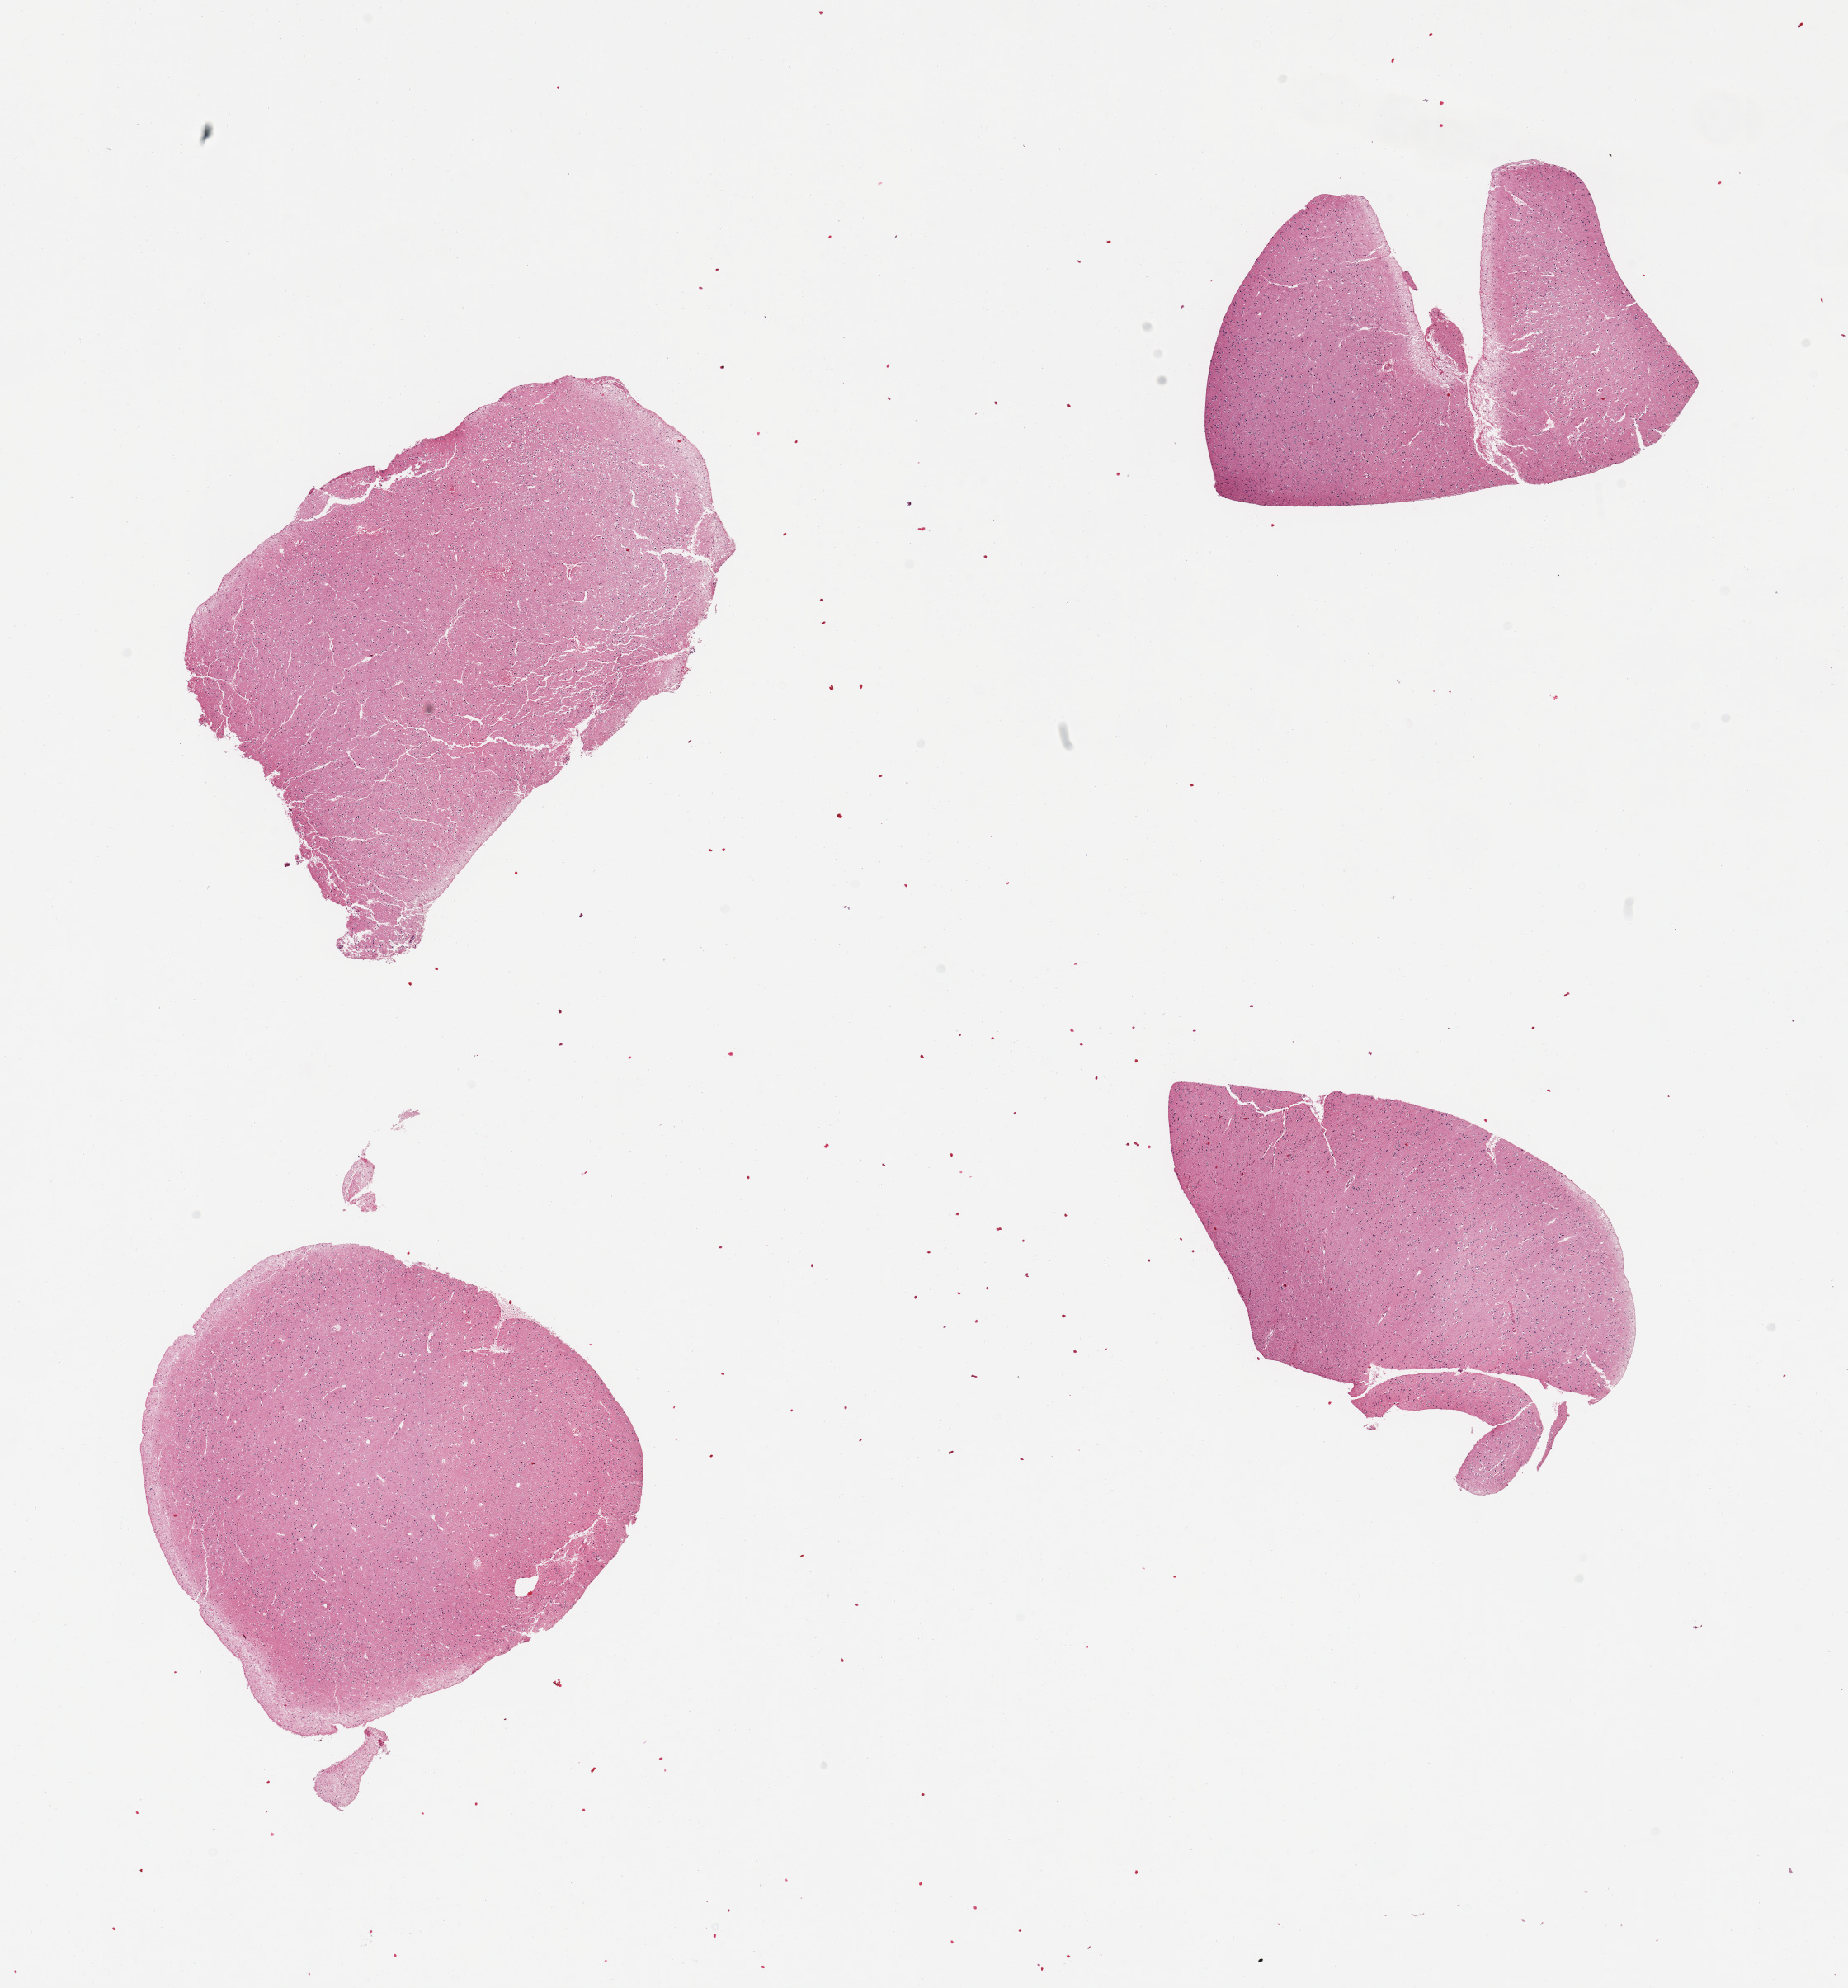
Haematoxylin and eosin whole-slide image — low-resolution overview of the scanned area, about 17.7 x 19.1 mm. PAXgene-fixed, paraffin-embedded tissue. Section of cerebral cortex (target tissue). Donor tissue sample. Donor: female.
Review note (as recorded): 4 pieces, no abnormalities.